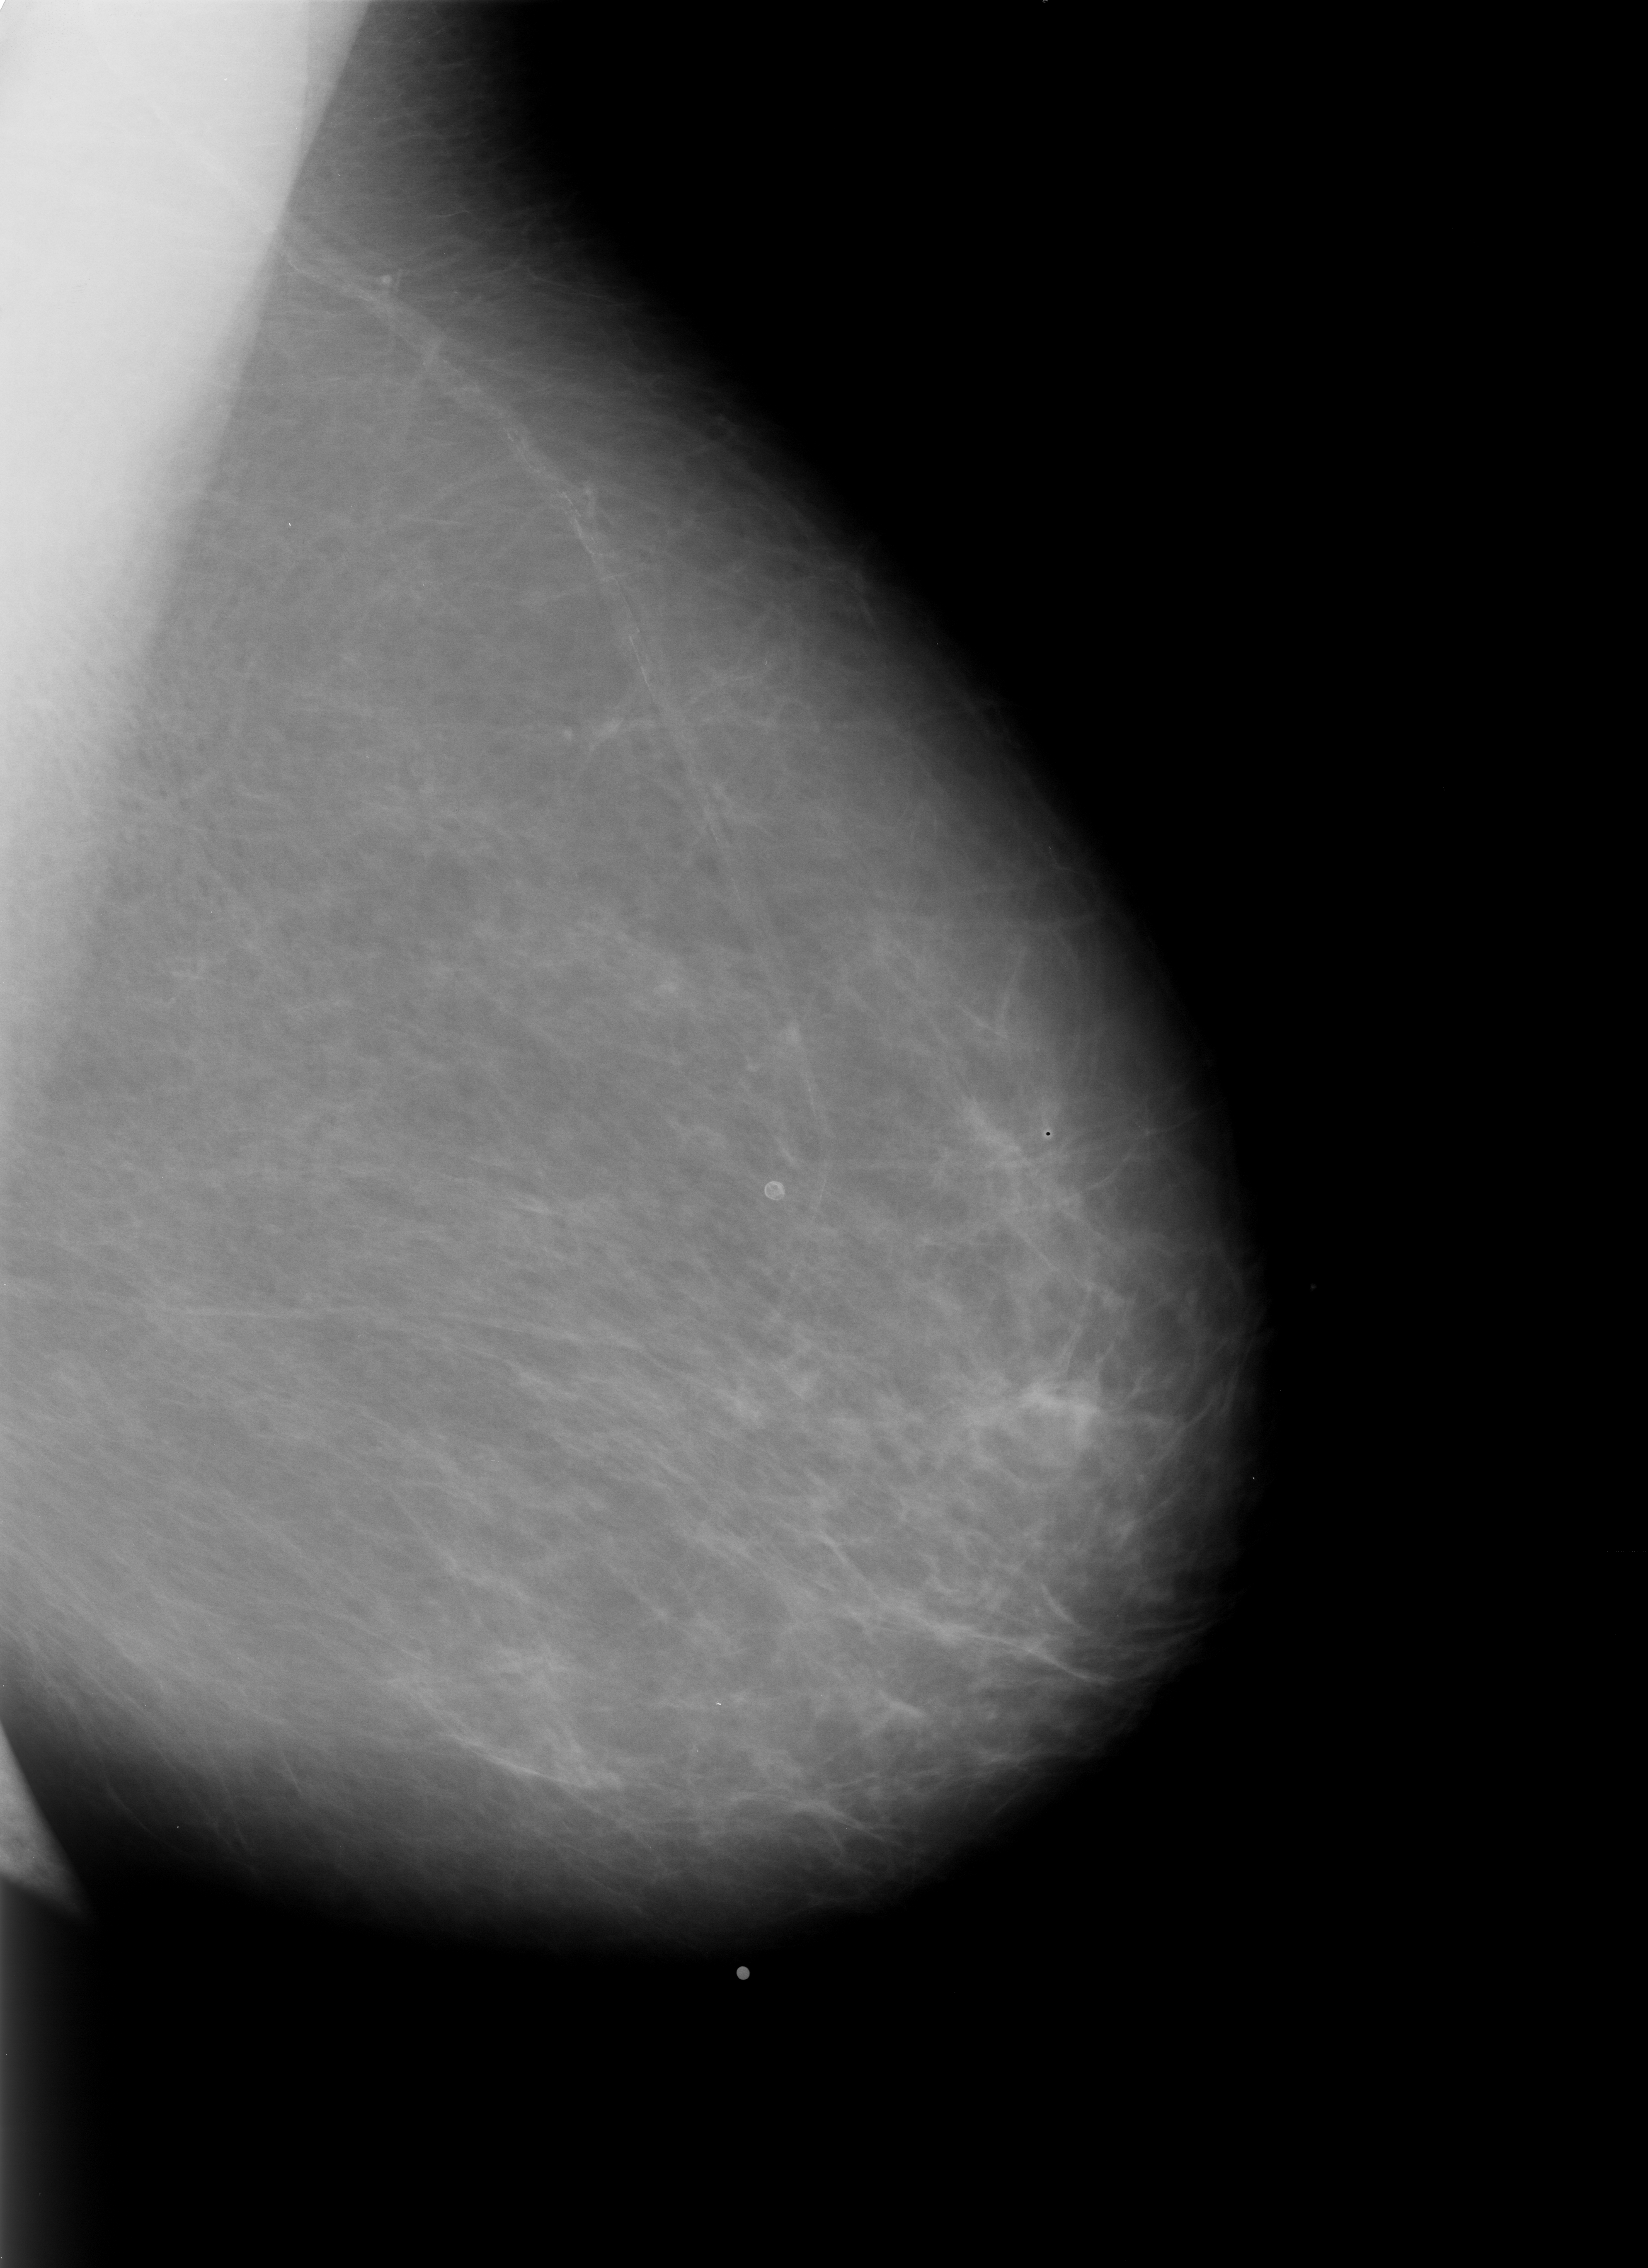
Digitized screen-film mammogram, left breast, MLO view, BI-RADS breast density category 1 (scale 1–4).
- Abnormality record for this image: calcifications, morphology lucent centered; BI-RADS assessment category 2; benign; no additional work-up was recommended (benign without callback).